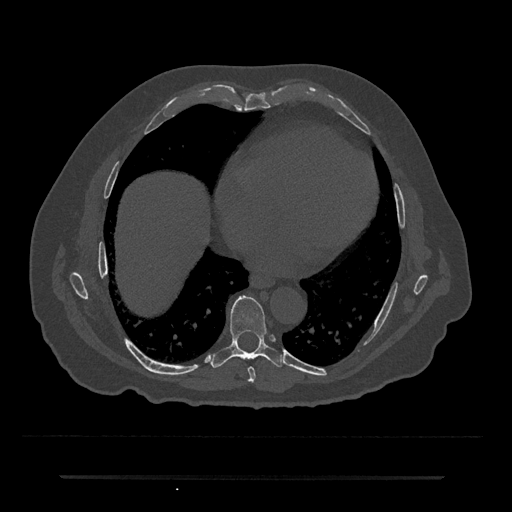
CT including the spine, one axial slice; position 341 of 797 along the scan axis; reconstruction kernel Br40s/3; 120 kVp; bone window (W 1800 / L 400 HU); 0.5 mm slice thickness; 512 × 512 image matrix, field of view 437 × 437 mm. Male patient, age 69 years. Case-level facts recorded for this patient, not image findings: primary cancer: prostate.
Structures marked on this image (semi-automatically segmented with operator editing):
- T7 vertebra: bounding box [x1, y1, x2, y2] px = [248, 367, 256, 382]
- T8 vertebra: [211, 295, 283, 368]